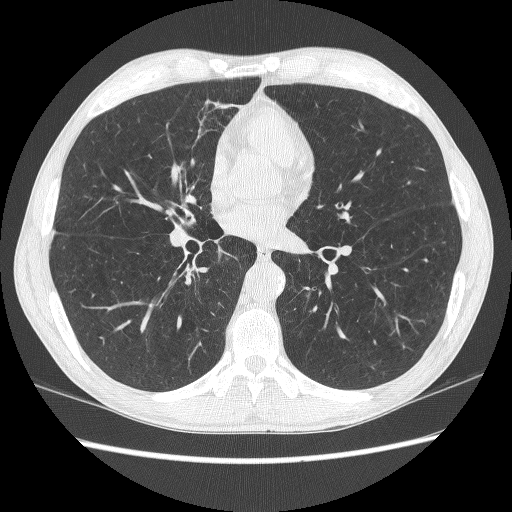
Chest CT (low-dose screening protocol), one axial image. First (baseline) screen. Lung window (W 1500 / L -600 HU). 1.25 mm slice thickness. Lung (sharp) reconstruction kernel (BONE). 120 kVp. 512 × 512 image matrix. Male participant, aged 62 years at enrolment. Former smoker at enrolment.
Expert reader's lesion annotation, bounding box [x1, y1, x2, y2] px = [328, 202, 364, 233]. Reader record for this screening exam (exam-level; its link to the box is not recorded): non-calcified nodule or mass ≥4 mm, right lower lobe, 8 × 4 mm, poorly defined margins, soft tissue attenuation, pre-existing on the prior screen: no. Note: the box lies in the patient's left hemithorax on this image, whereas the reader's record names the right lung; they may be different findings.